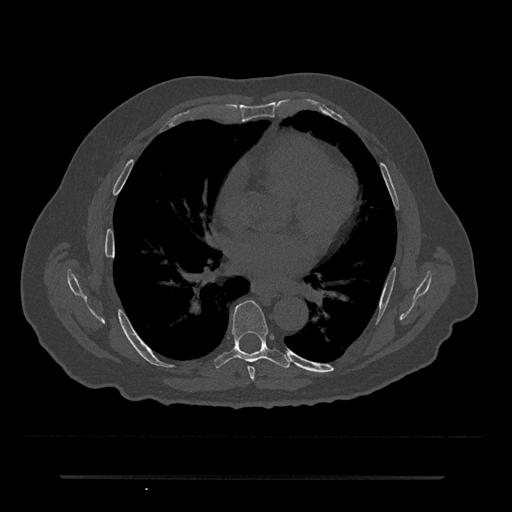
CT including the spine, one axial slice. Slice 393 of 797 in the series (ordered by position). Reconstruction kernel Br40s/3. 120 kVp. Bone window (W 1800 / L 400 HU). 0.5 mm slice thickness. 512 × 512 image matrix, field of view 437 × 437 mm. Male patient, age 69 years. From the clinical record (not read from this slice): primary cancer: prostate.
Outlined on this slice (semi-automatic segmentation, software-assisted and operator-edited):
- T6 vertebra: box from (x=248, y=366) to (x=255, y=380) px
- T7 vertebra: (x=214, y=300)–(x=290, y=368)